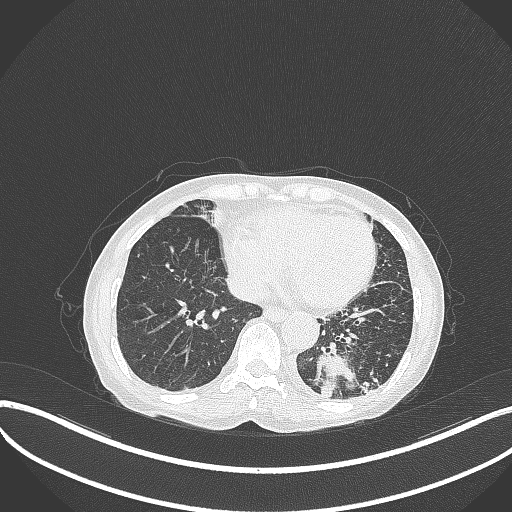
Chest CT, one axial slice; slice 90 of 370 in the series (ordered by position); lung window (W 1500 / L -600 HU); 512 × 512 image matrix, field of view 400 × 400 mm. Patient: female, 78 years. Case-level facts recorded for this patient, not image findings: clinical TNM (as recorded): T3 N0 M1.
Annotated regions visible in this slice (bounding box drawn by a radiologist):
- lung tumour (recorded histology: squamous cell carcinoma): bounding box [x1, y1, x2, y2] px = [312, 342, 362, 400]